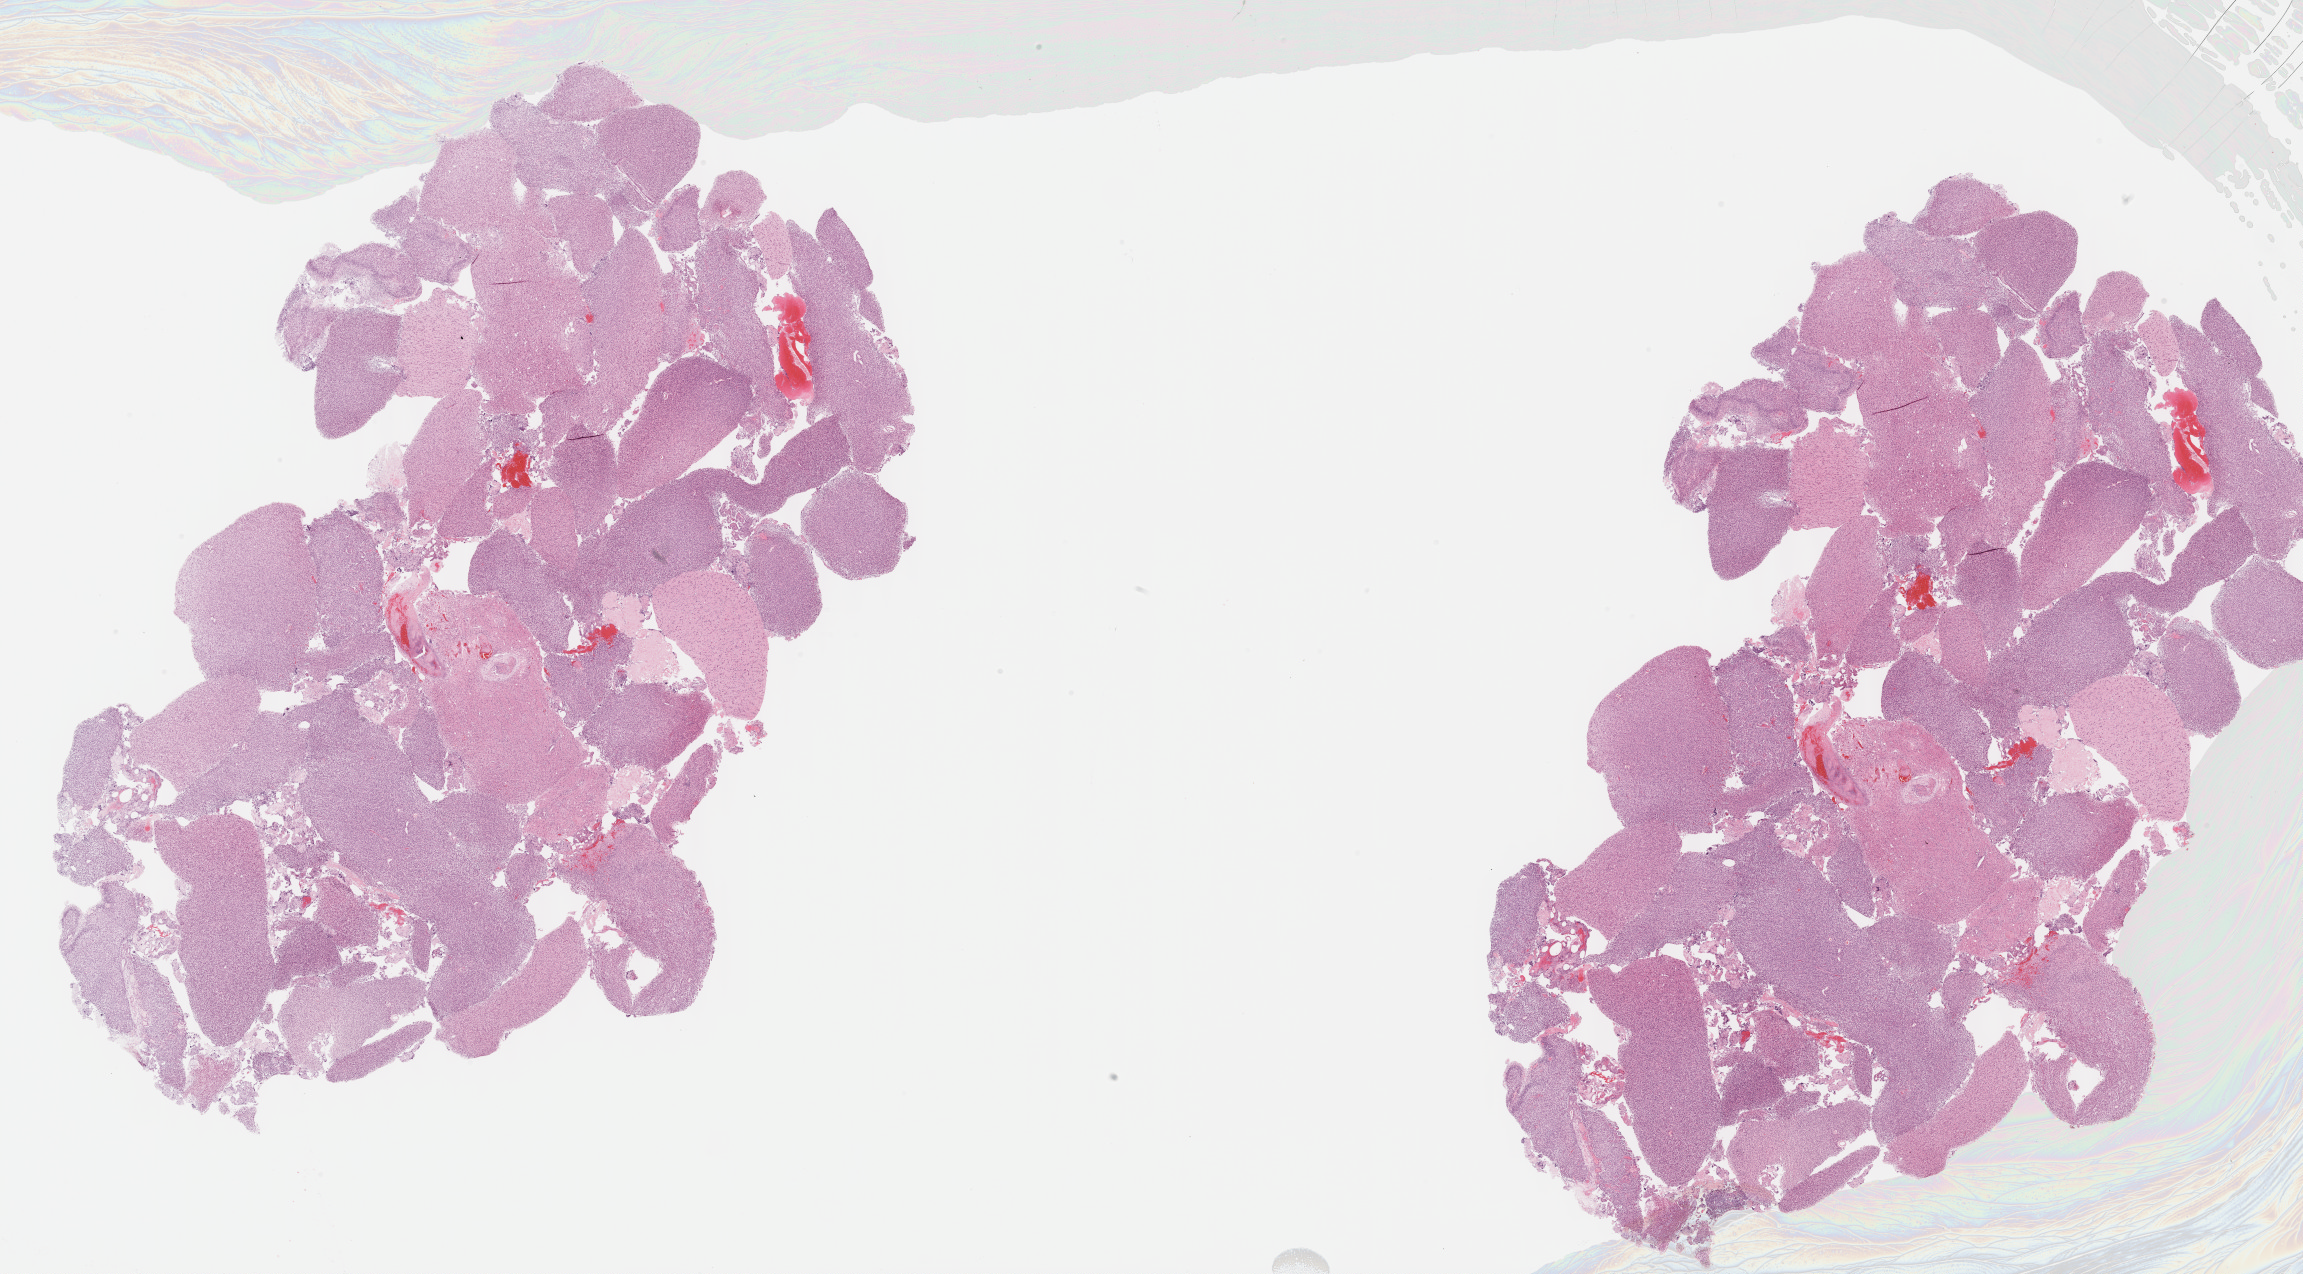
Whole-slide histology image, Hematoxylin and eosin (H&E) stained — a low-resolution overview of the entire scanned area, about 37.2 x 20.6 mm (slide scanned at 40x), formalin-fixed paraffin-embedded (FFPE) diagnostic section, sample: primary tumour, brain. Male patient; age at initial diagnosis 49 years.
Diagnosis: Glioblastoma.